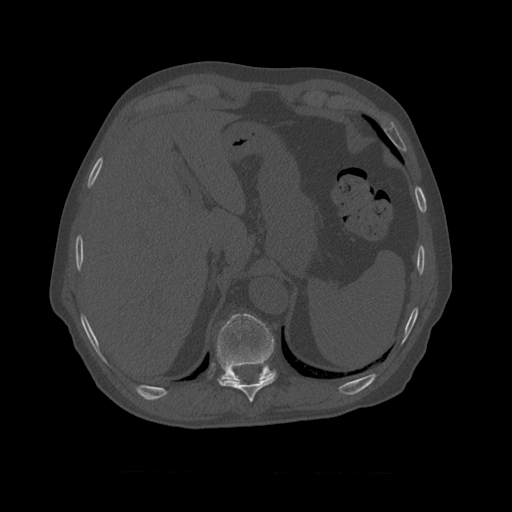
CT including the spine, one axial slice. Position 414 of 450 along the scan axis. Reconstruction kernel STANDARD. Bone window (W 1800 / L 400 HU). 1.25 mm slice thickness. 512 × 512 image matrix. Patient age 75 years. Case-level facts recorded for this patient, not image findings: primary cancer: prostate.
Annotated regions visible in this slice (semi-automatic segmentation, software-assisted and operator-edited):
- T10 vertebra: bounding box [x1, y1, x2, y2] px = [214, 313, 277, 382]
- T9 vertebra: [217, 375, 277, 403]